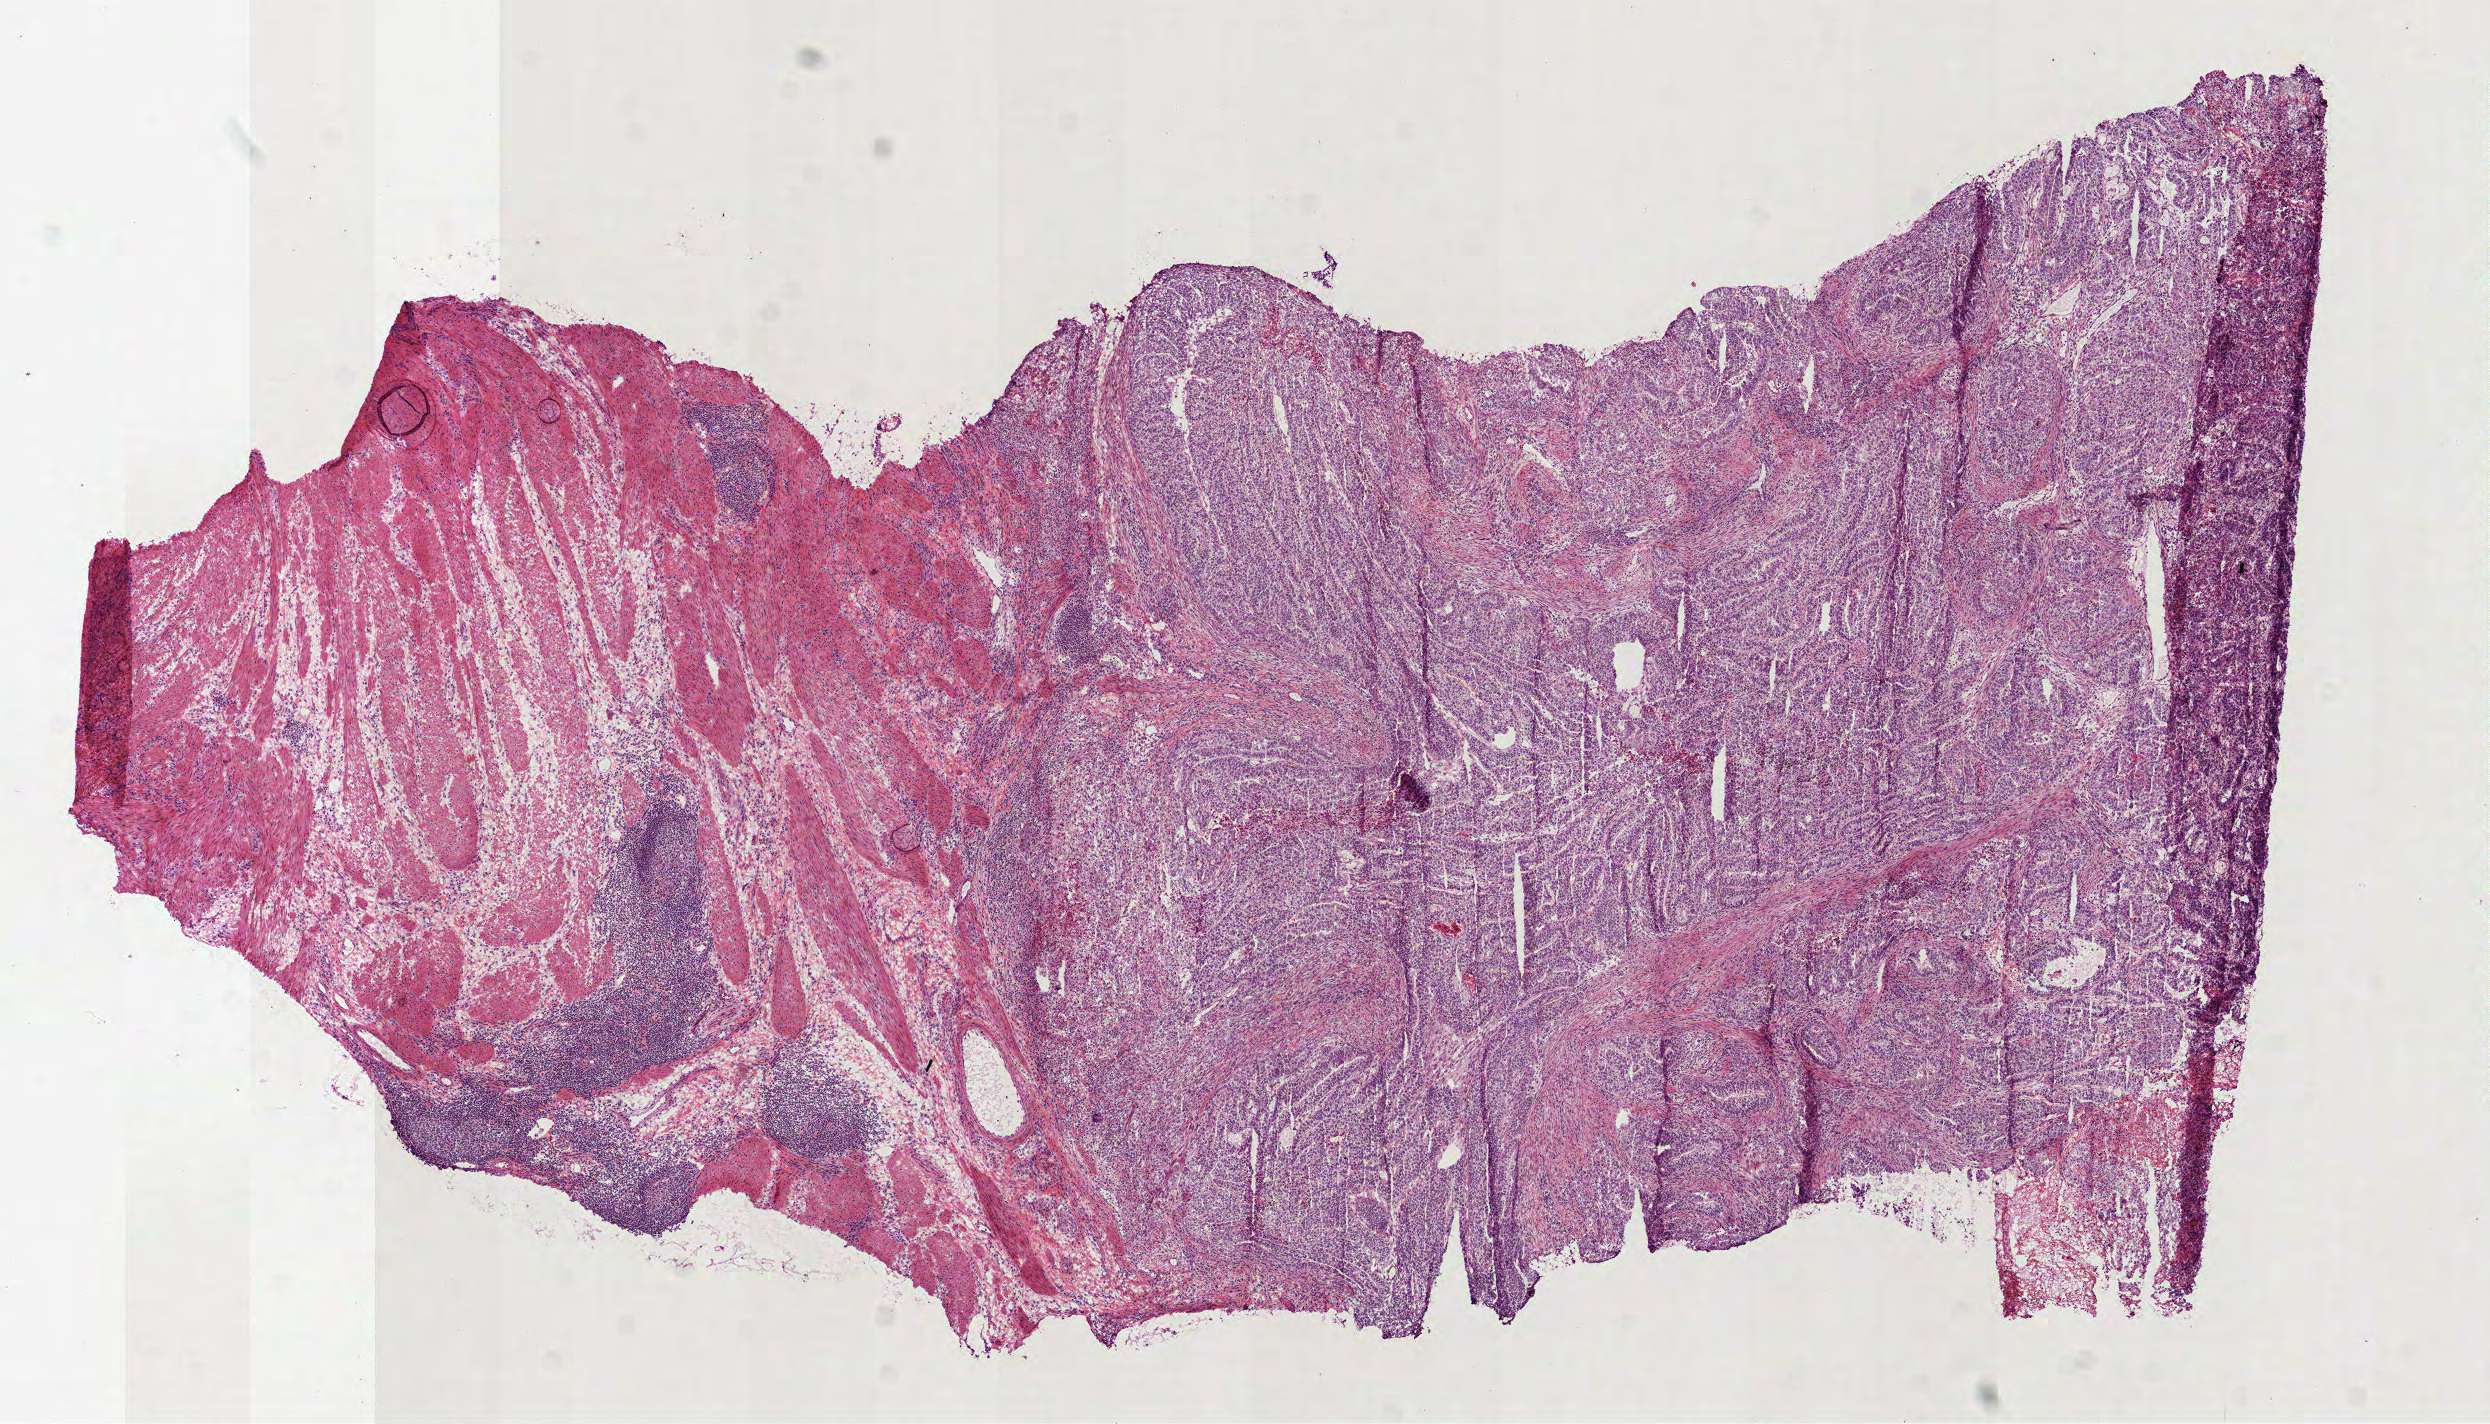
Digitized Hematoxylin and eosin (H&E) stained tissue section (whole slide), low-resolution overview of the scanned area, about 10.0 x 5.7 mm; frozen section from the bottom of the tissue portion; primary tumour sample from the stomach. Male, age 57 years at initial diagnosis. Histologic grade: G2 (moderately differentiated). Slide review estimates, as recorded: tumour cells 59%, tumour nuclei 75%, normal cells 35%, stromal cells 0%, necrosis 6%. Inflammatory infiltration, as recorded: lymphocyte infiltration 15%, monocyte infiltration 0%, neutrophil infiltration 0%.
Lymph nodes positive (case pathology): 6 of 10 examined. AJCC pathologic stage: IIB (7th edition). Histologic diagnosis: Adenocarcinoma, NOS.